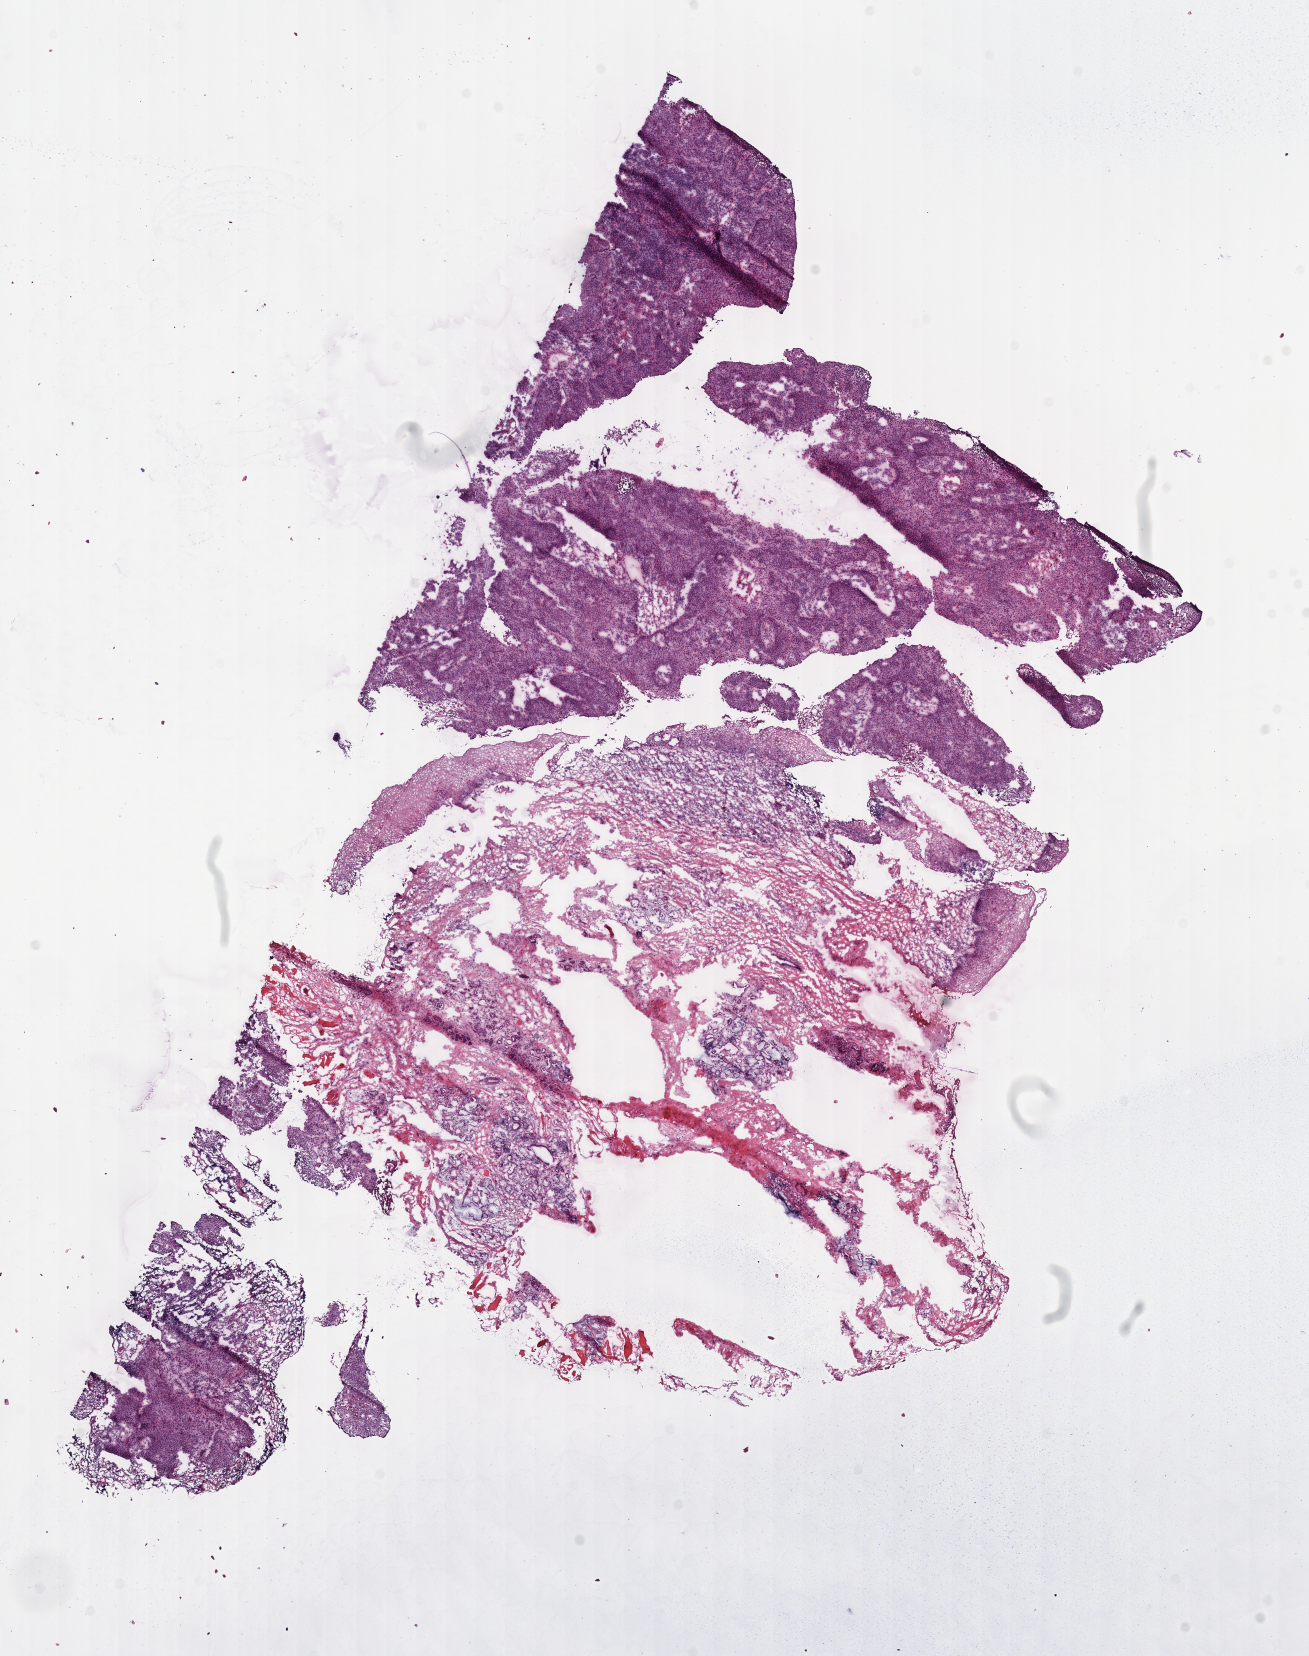
Whole-slide histology image, H&E-stained — a low-resolution overview of the entire scanned area, about 10.3 x 13.0 mm. Frozen section from the top of the tissue portion. Head and neck, primary tumour sample. Male, age 47 years at initial diagnosis. Slide review estimates, as recorded: tumour cells 50%, tumour nuclei 65%.
Histologic diagnosis: Squamous cell carcinoma, NOS (base of tongue, NOS).